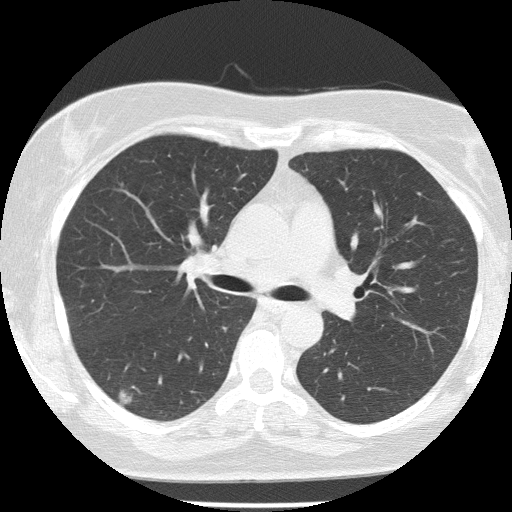
Low-dose screening chest CT, axial slice, baseline annual screen, lung window (W 1500 / L -600 HU), lung (sharp) reconstruction kernel (FC51), 120 kVp, slice 60 of 142 in the series, 512 × 512 image matrix, field of view 303 × 303 mm. Female participant, aged 58 years at enrolment. Former smoker at enrolment.
Expert reader's lesion annotation, box from (x=97, y=370) to (x=151, y=423) px. The screening reader recorded 2 non-calcified nodules or masses ≥4 mm on this exam; which of them this box marks is not recorded.